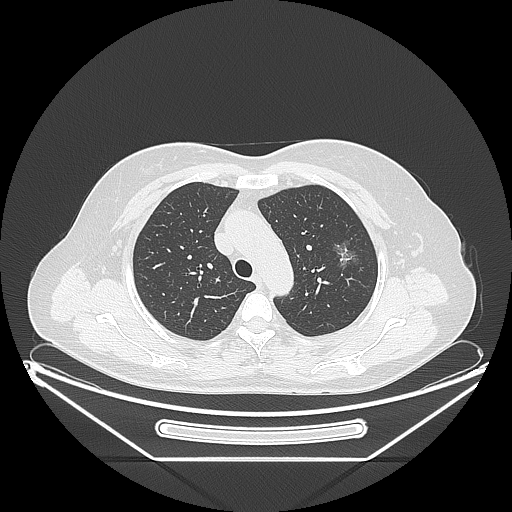
Chest CT, one axial slice. Slice 162 of 226 in the series (ordered by position). Reconstruction kernel LUNG. 120 kVp. Lung window (W 1500 / L -600 HU). 1.25 mm slice thickness. 512 × 512 image matrix, field of view 447 × 447 mm. Patient: female, 54 years. From the clinical record (not read from this slice): clinical TNM (as recorded): T1c N0 M0; histopathological grade: G1.
Structures marked on this image (rectangle marked by the reading radiologist):
- lung tumour (recorded histology: adenocarcinoma): box from (x=328, y=236) to (x=365, y=277) px